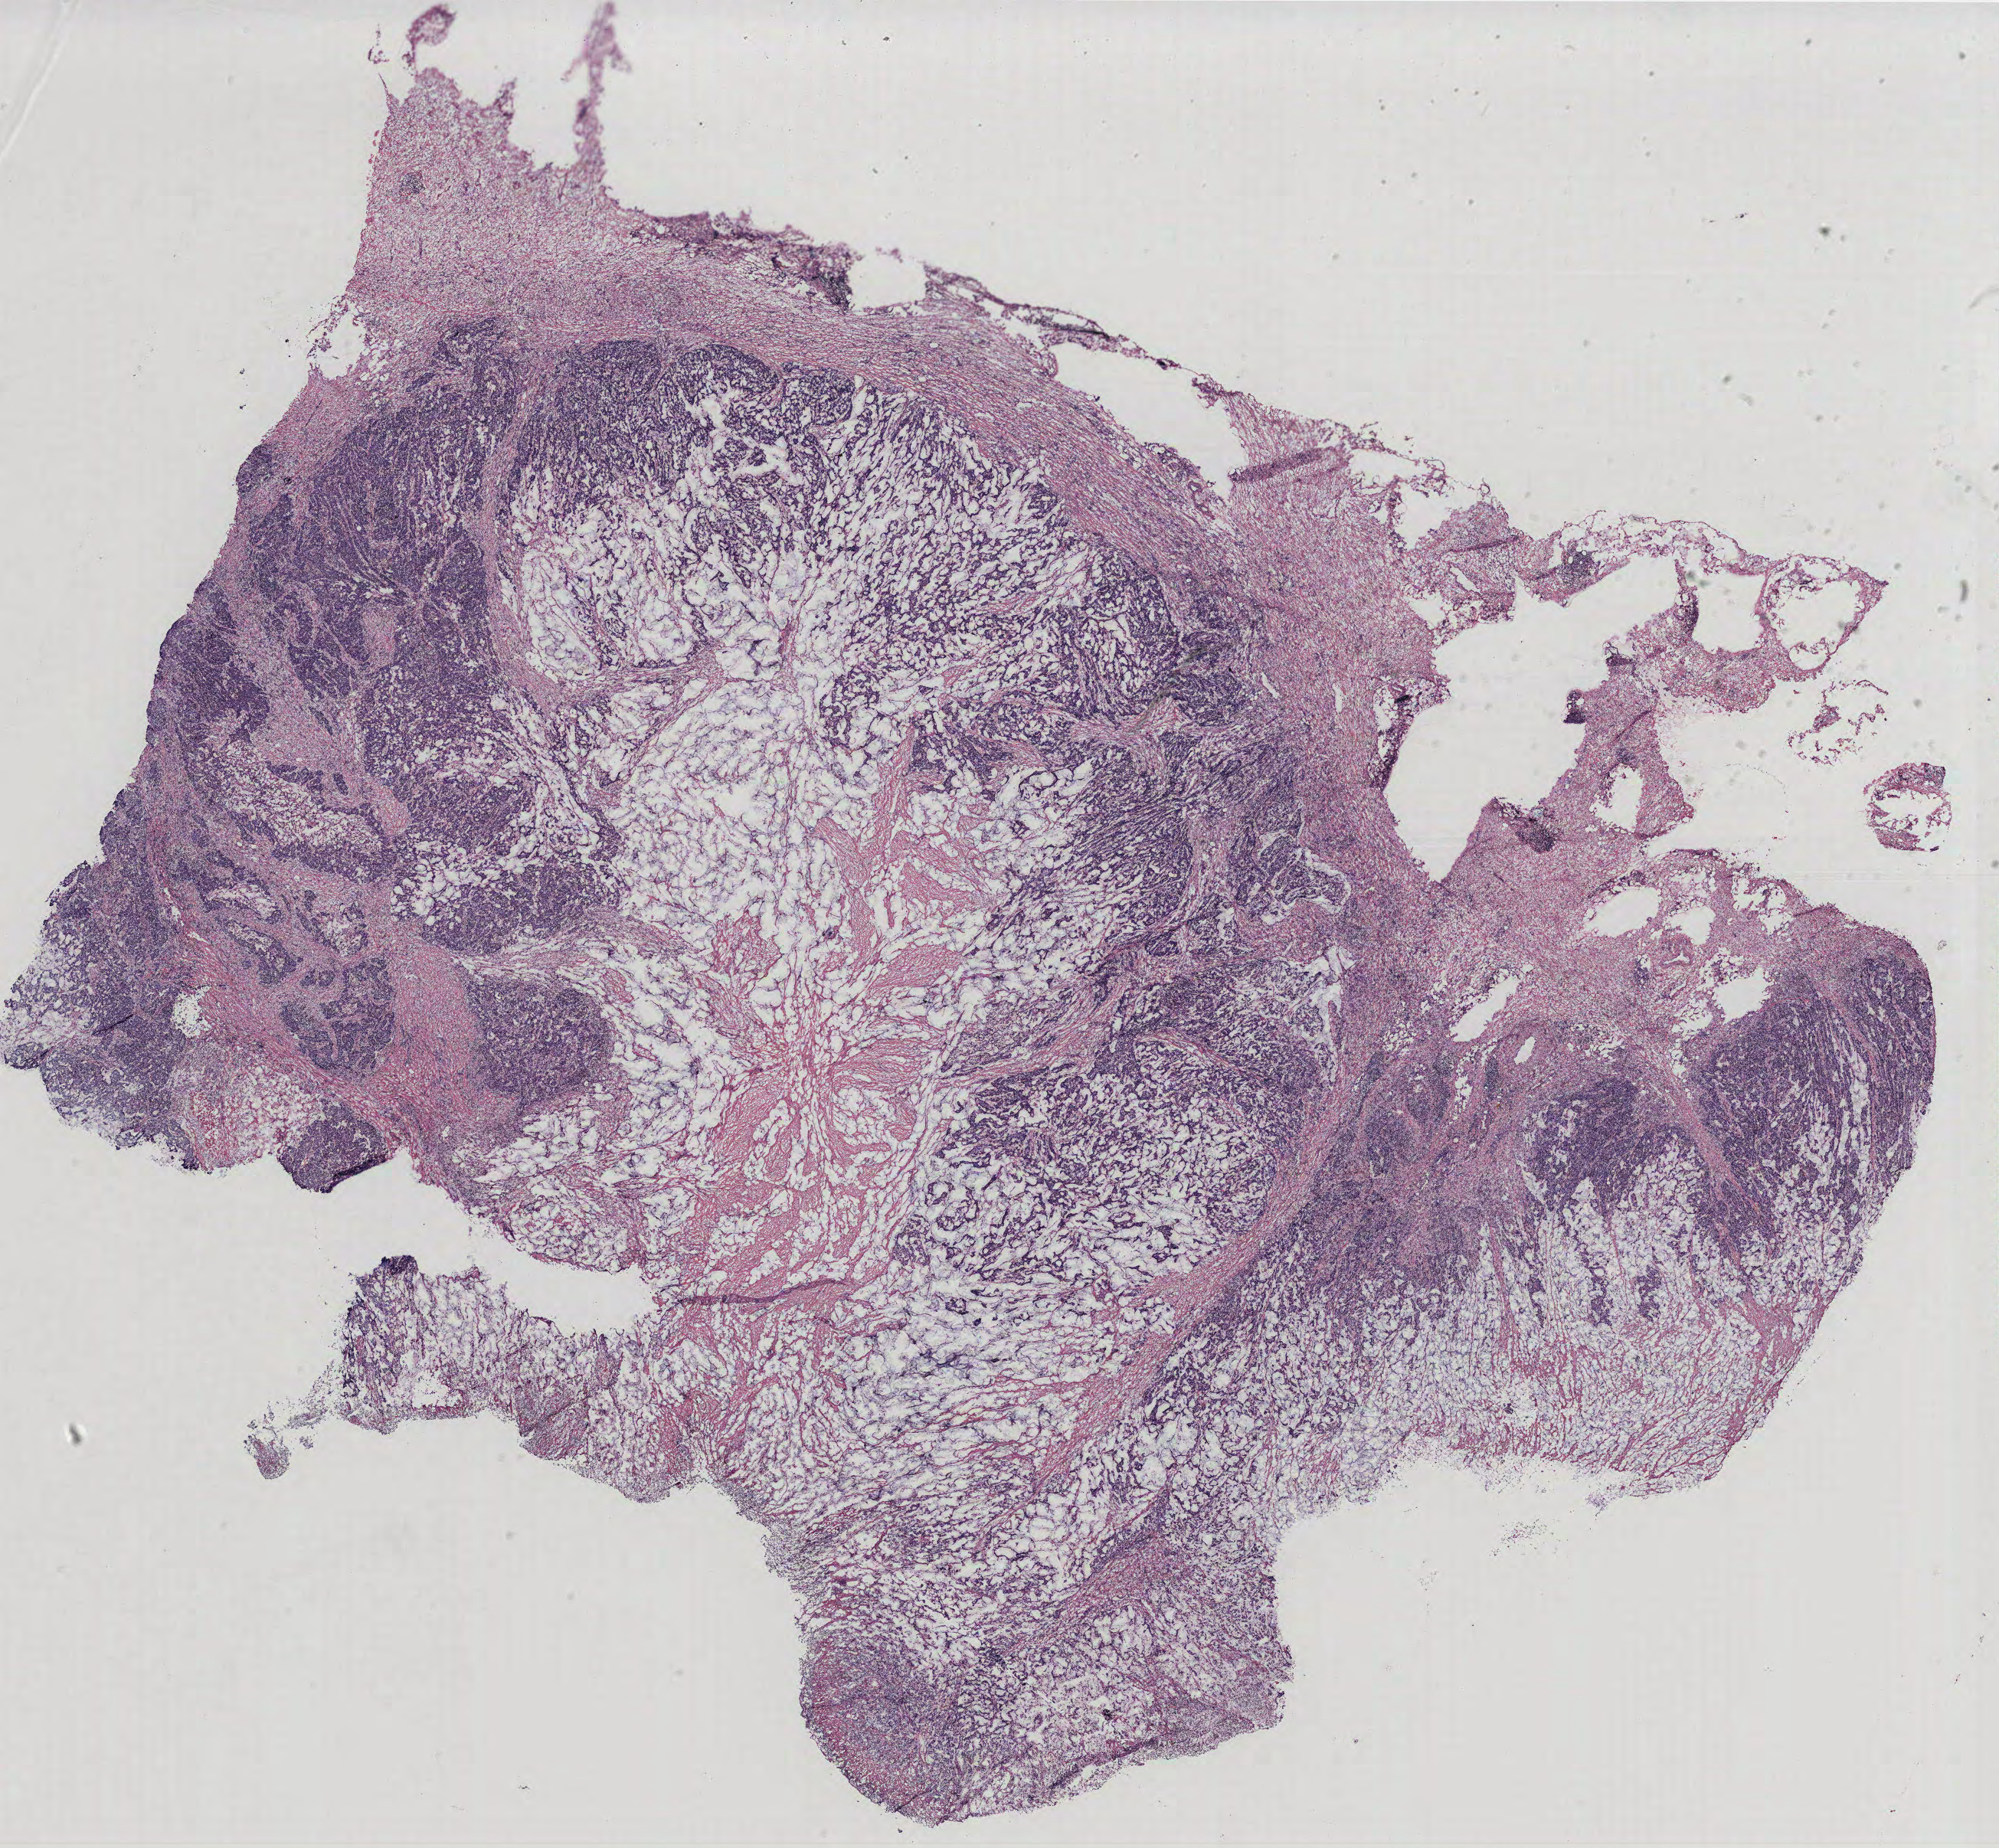
Whole-slide histology image, H&E, low-resolution overview of the scanned area, about 20.9 x 19.3 mm (from a 40x scan), colon, normal (non-tumour) tissue. Patient: male, age 36 years.
This section: normal (non-tumour) tissue from the same patient. Patient diagnosis: Adenocarcinoma, NOS.